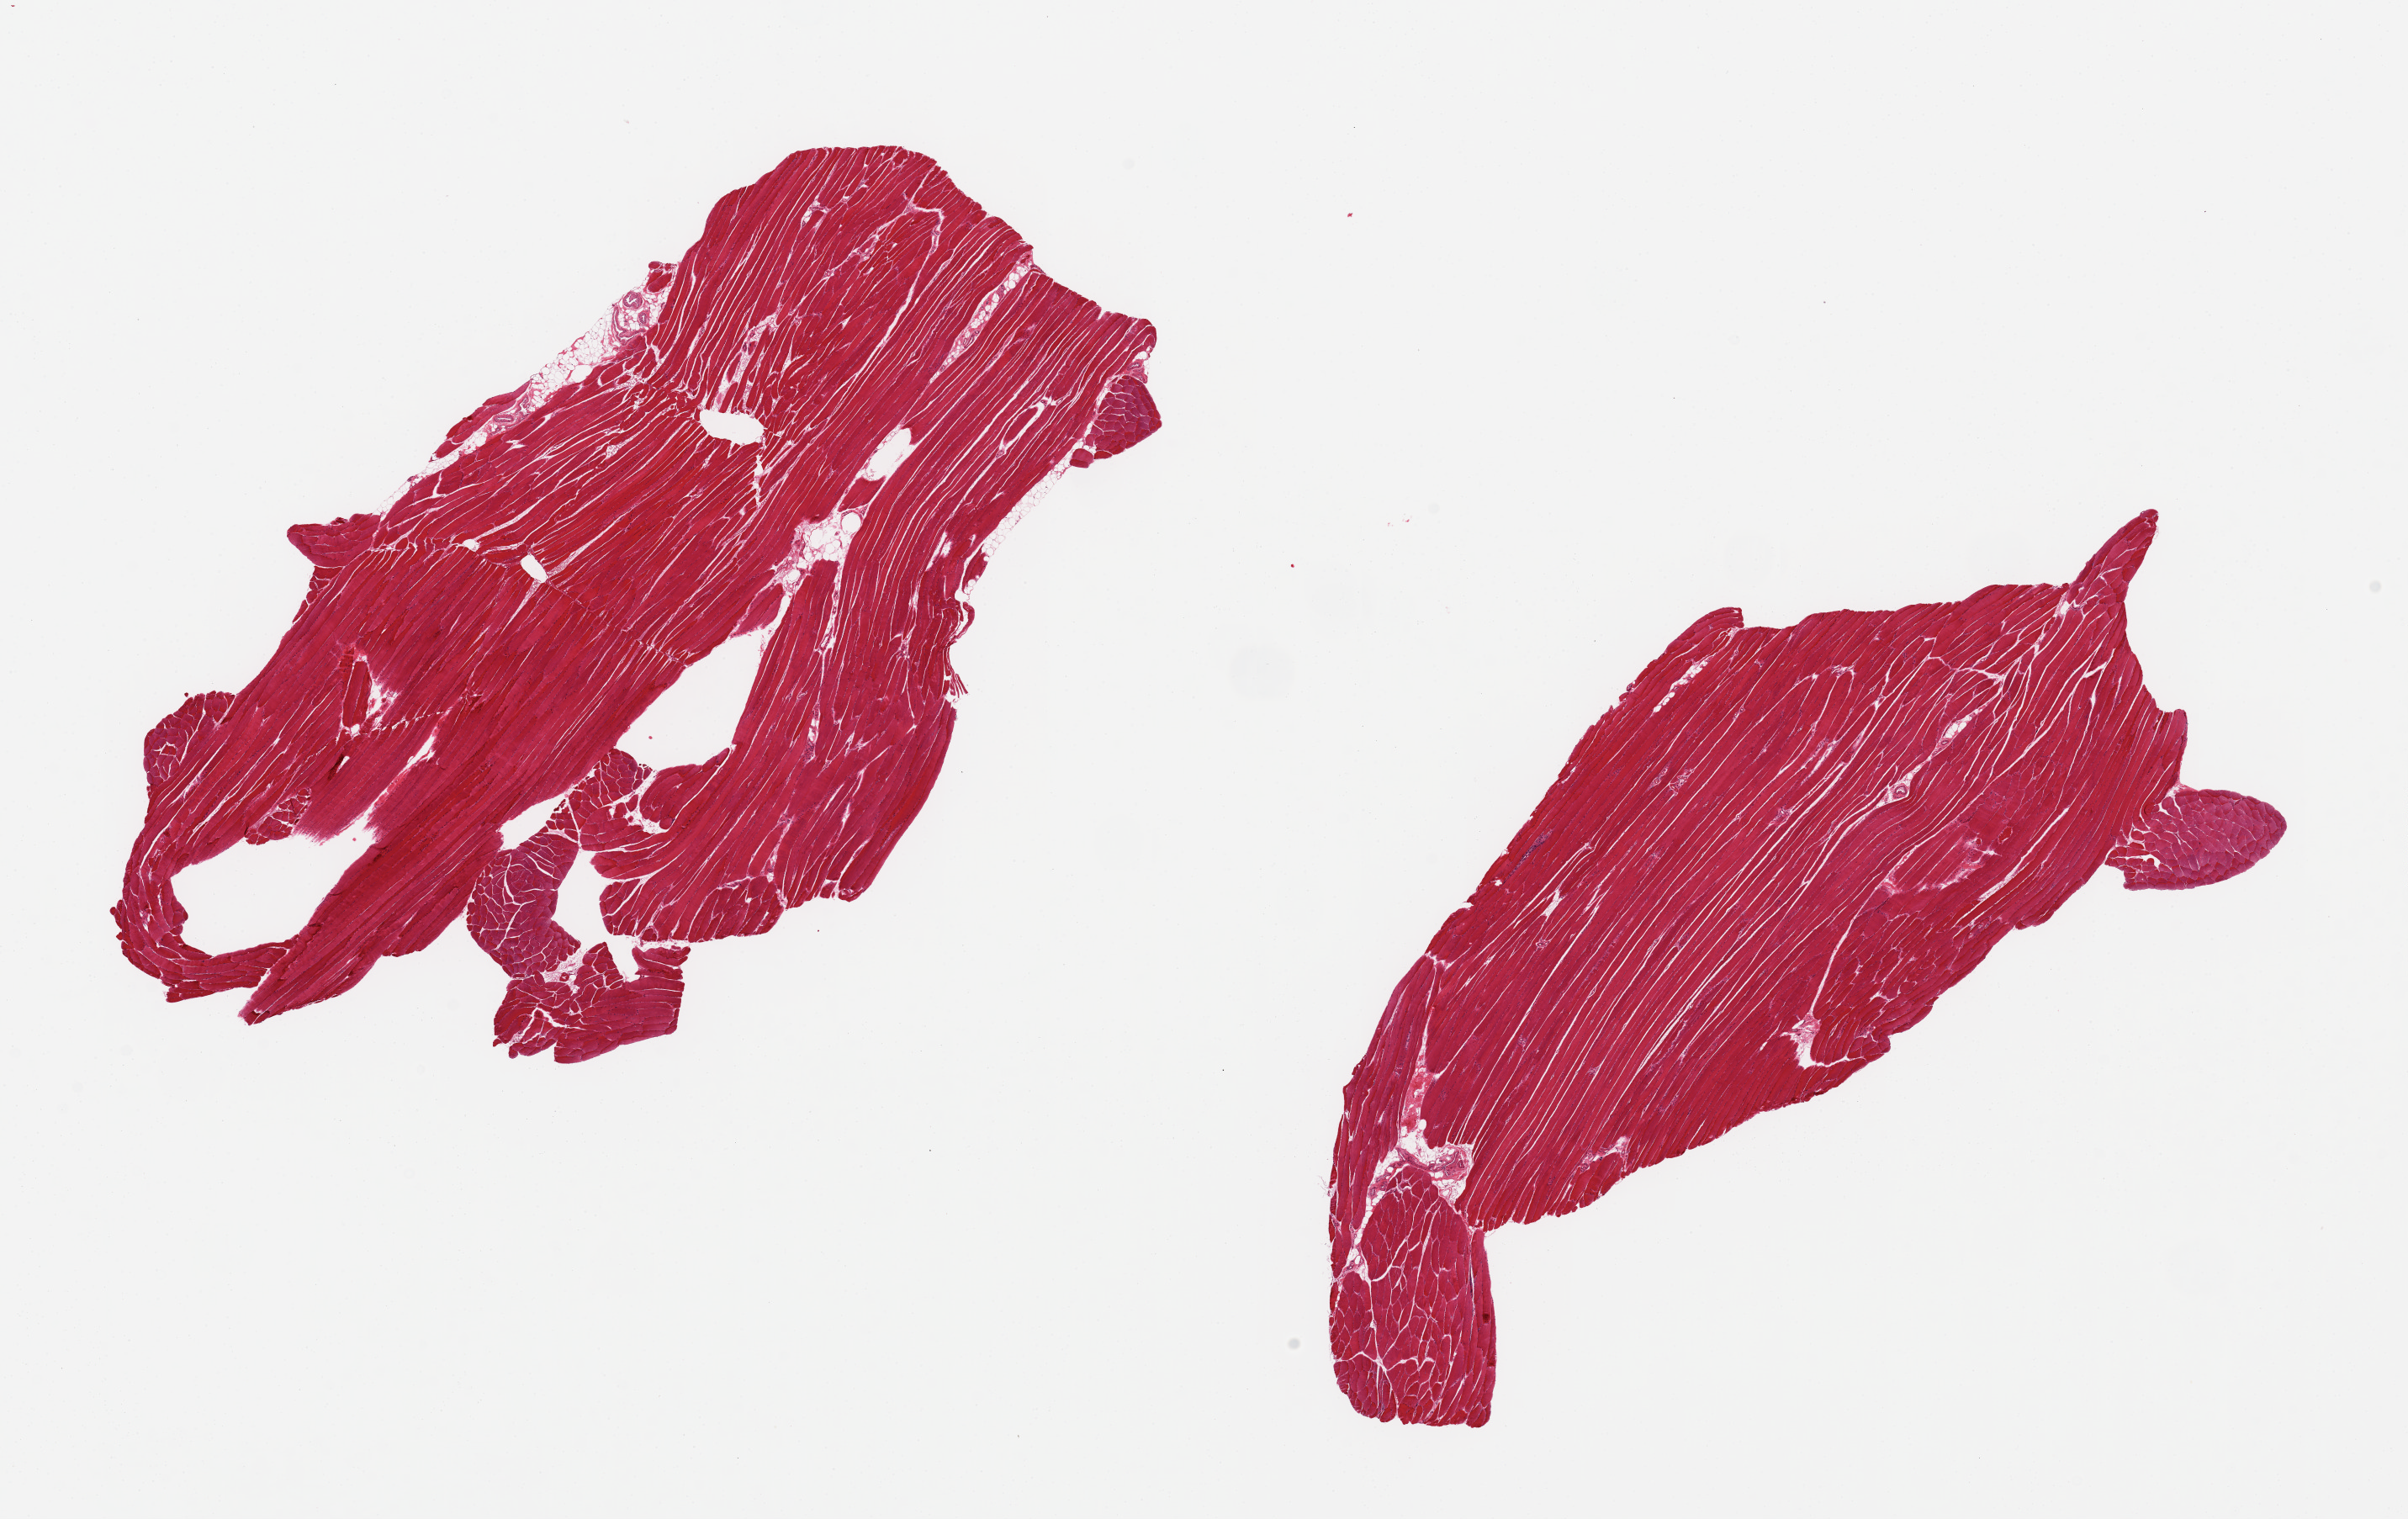
Digitized hematoxylin and eosin (H&E)-stained section, low-resolution overview of the scanned area, about 22.6 x 14.3 mm (slide scanned at 20x), PAXgene-fixed, paraffin-embedded tissue, section of skeletal muscle (target tissue), tissue donor sample. Donor: male.
Review note (as recorded): 2 pieces, fat is < 5% total.